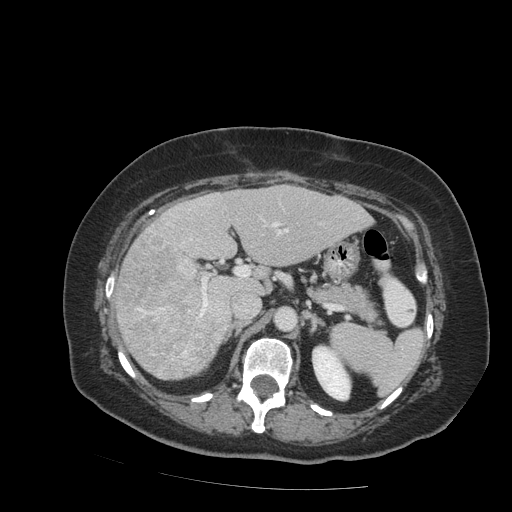
Contrast-enhanced abdominal CT (liver protocol), one axial slice. Position 48 of 99 along the scan axis. Reconstruction kernel STANDARD. Soft-tissue window (W 400 / L 40 HU). 2.5 mm slice thickness. 512 × 512 image matrix. From the clinical record (not read from this slice): diagnosis: hepatocellular carcinoma (patient treated with transarterial chemoembolisation; whether this scan precedes or follows treatment is not stated here); TNM stage (as recorded): Stage-IVB; Child-Pugh class: A; tumour differentiation: moderately differentiated.
Structures marked on this image (semi-automatically segmented with operator editing):
- liver parenchyma outside the tumour (the mass and vessels are separate outlines, so this box may not span the whole liver): bounding box [x1, y1, x2, y2] px = [114, 184, 372, 378]
- mass: [116, 234, 226, 377]
- liver vessels: [189, 209, 289, 313]